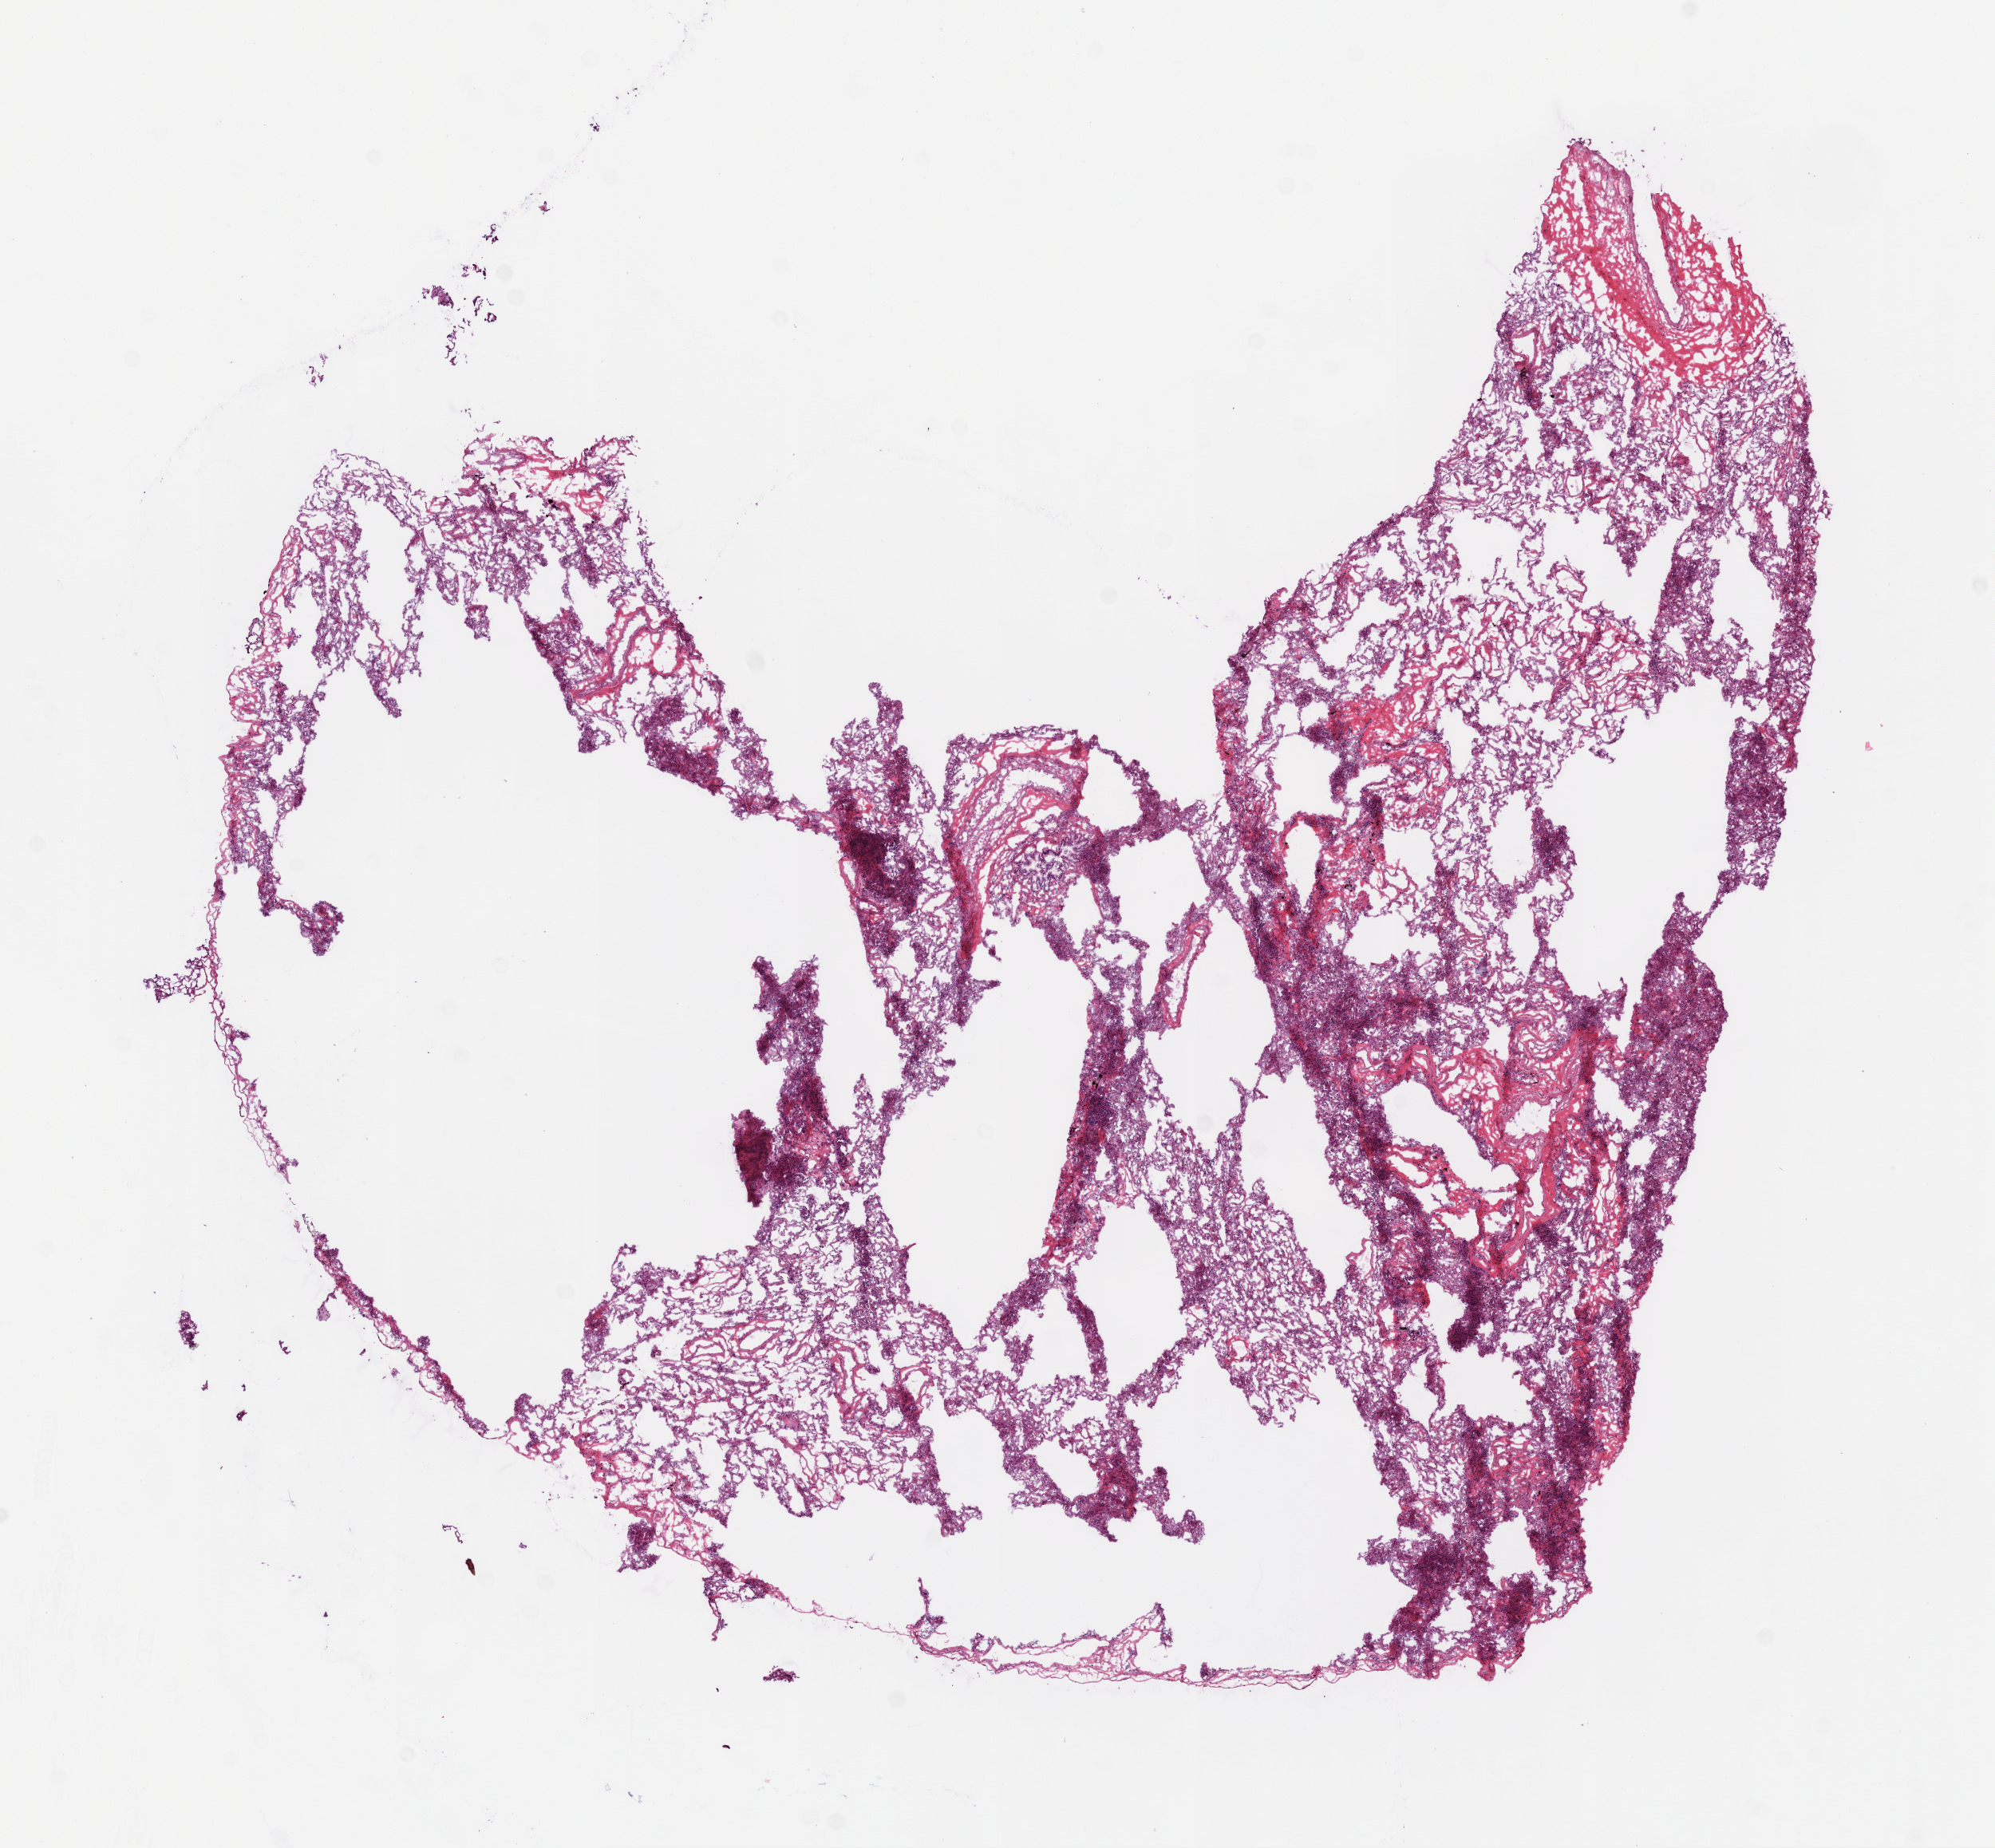
H&E whole-slide image, a low-resolution overview of the entire scanned area, about 10.0 x 9.3 mm (acquisition: 20x scan), frozen section, sample: solid tissue normal (non-tumour tissue), lung. Patient: female, age at initial diagnosis 62 years.
* this section: solid tissue normal sample (biorepository sample class)
* patient diagnosis: Squamous cell carcinoma, NOS (upper lobe, lung)